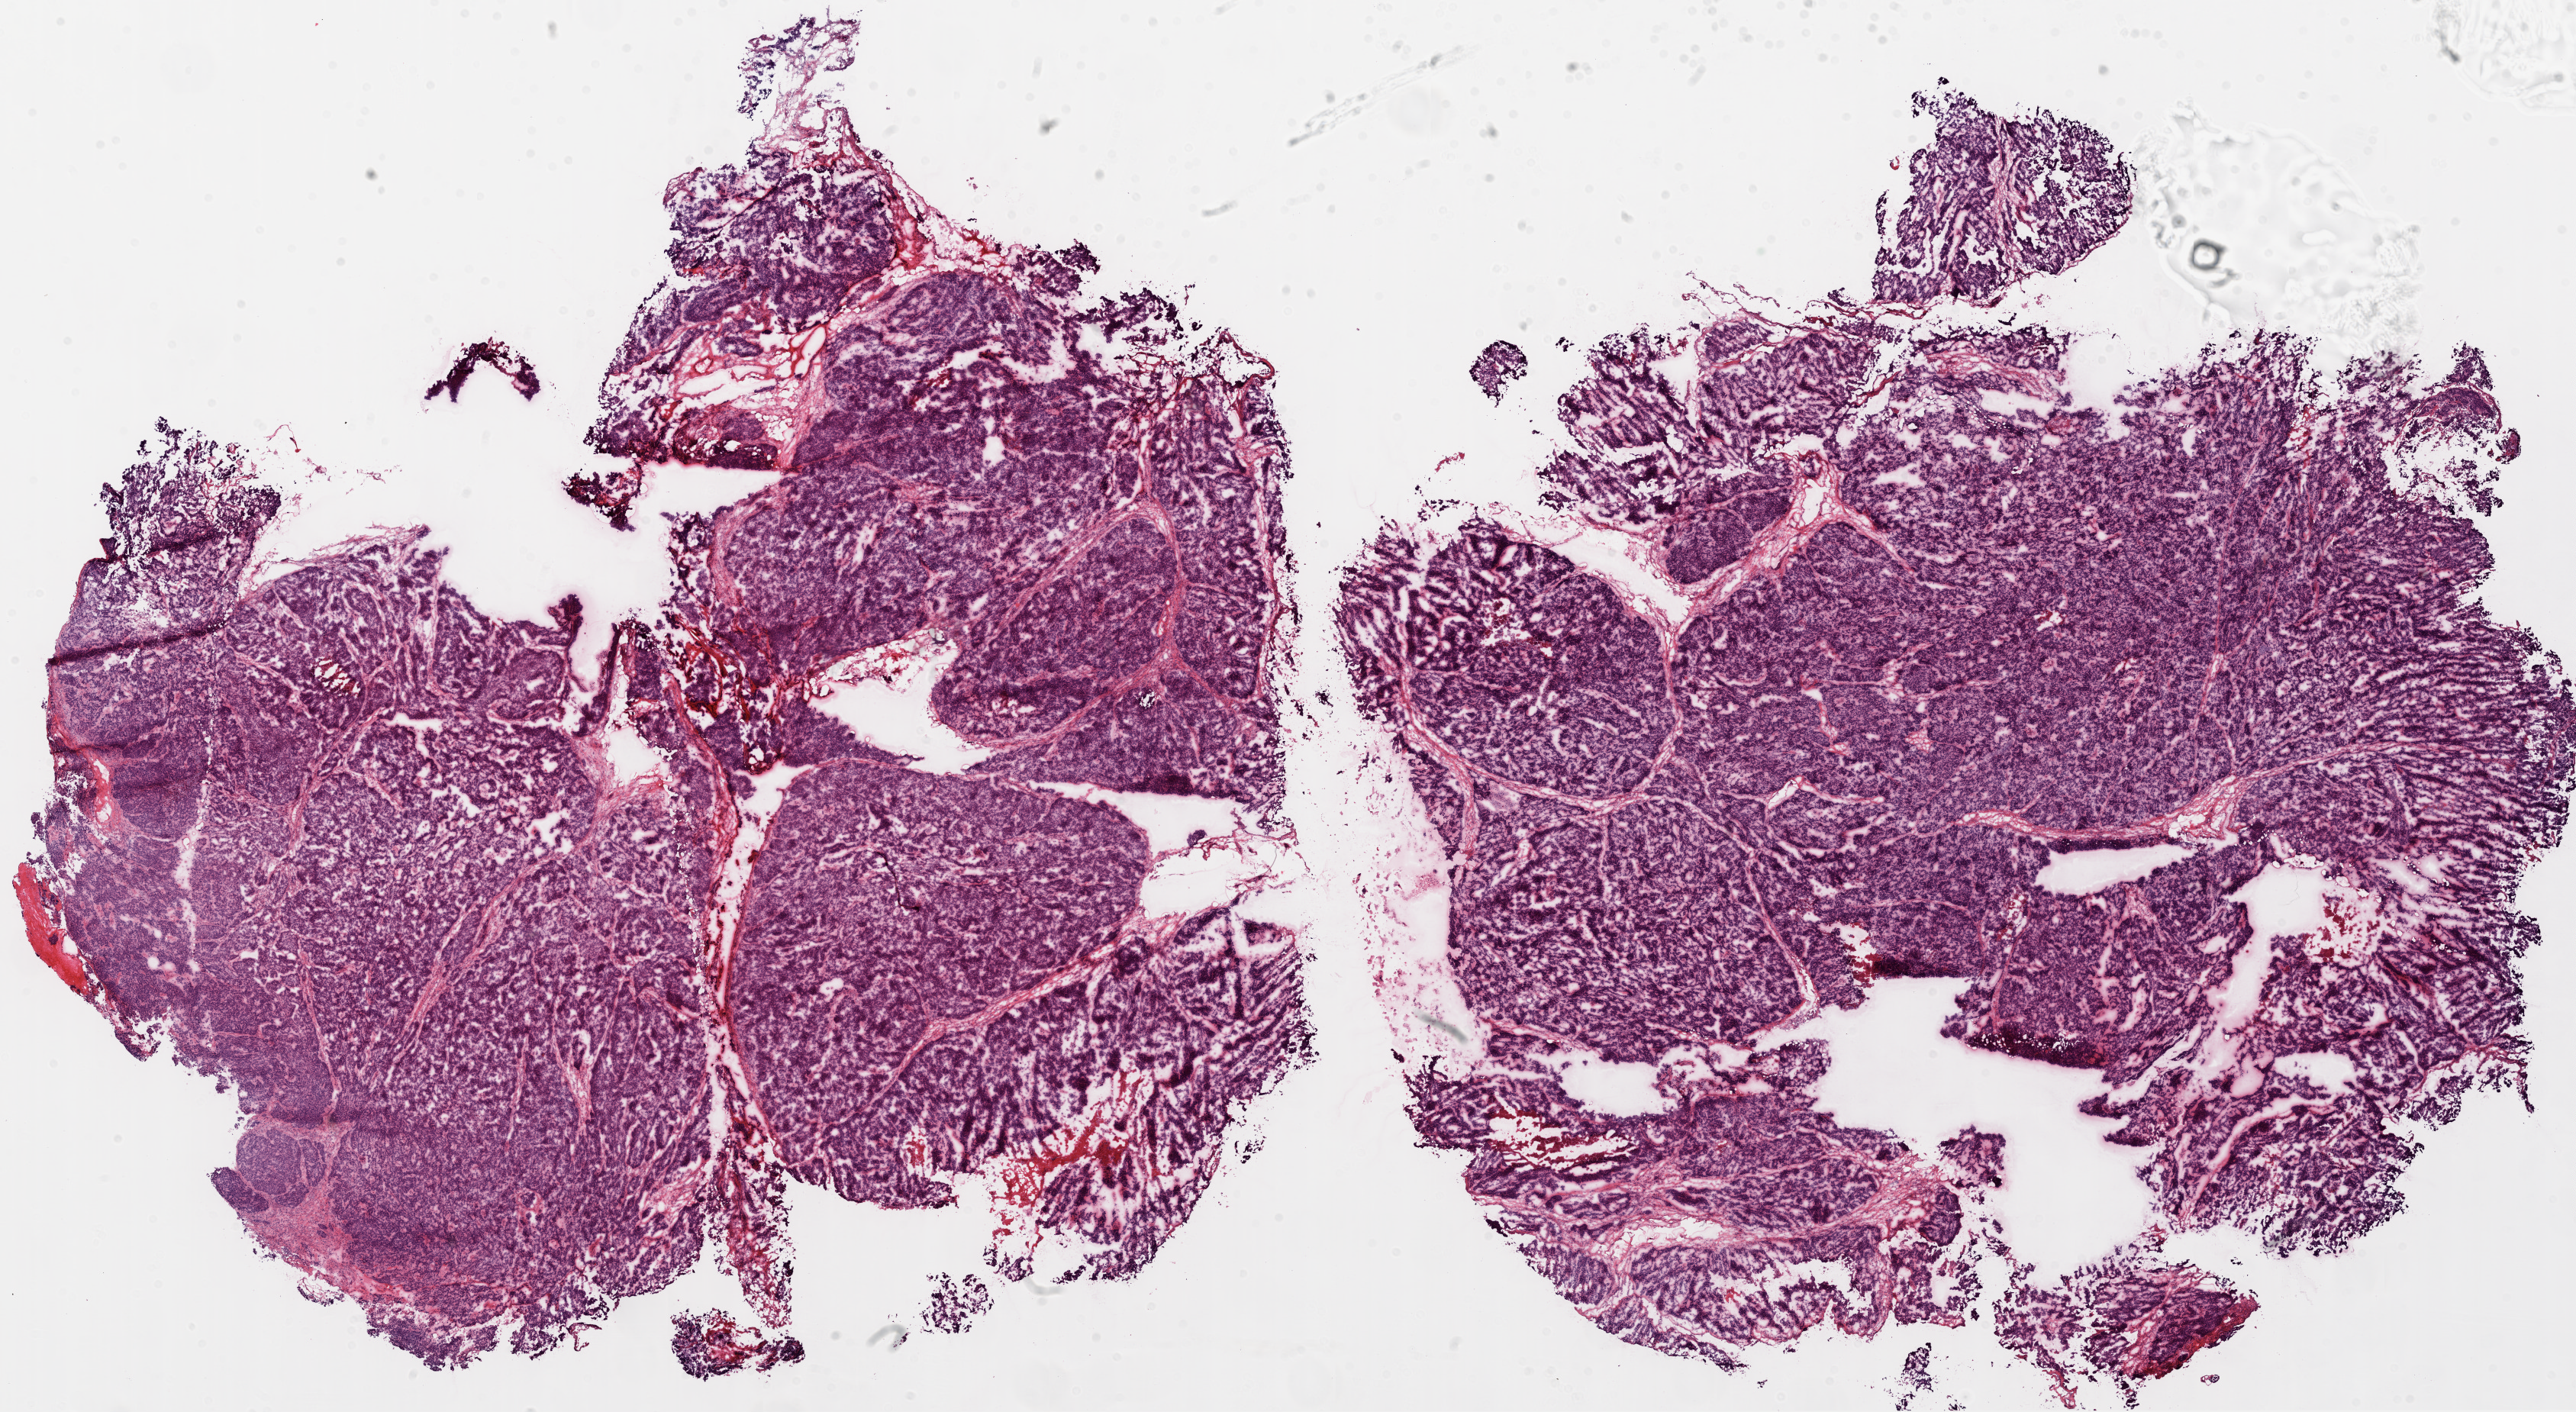
Digitized H&E-stained tissue section (whole slide) — shown as a low-resolution overview of the whole scanned area (about 27.1 x 14.8 mm, from a 20x scan), frozen section, primary tumour sample from the ovary. Female patient; age at initial diagnosis 66 years. Histologic grade: G3 (poorly differentiated). Composition of this section per pathologist review: tumour cells 94%, tumour nuclei 99%, normal cells 0%, stromal cells 1%, necrosis 5%.
Pathologic diagnosis: Serous cystadenocarcinoma, NOS. FIGO stage: IIIC.